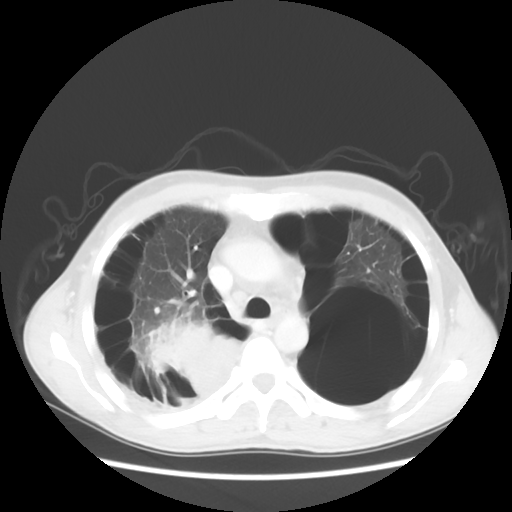
Chest CT, one axial slice. Position 38 of 56 along the scan axis. Reconstruction kernel STANDARD. 140 kVp. Lung window (W 1500 / L -600 HU). 5 mm slice thickness. 512 × 512 image matrix, field of view 351 × 351 mm. Male patient, age 41 years. Case-level facts recorded for this patient, not image findings: clinical TNM (as recorded): T4 N0 M1a; histopathological grade: G3.
Structures marked on this image (rectangle marked by the reading radiologist):
- lung tumour (recorded histology: large cell carcinoma): bounding box [x1, y1, x2, y2] px = [144, 317, 239, 396]